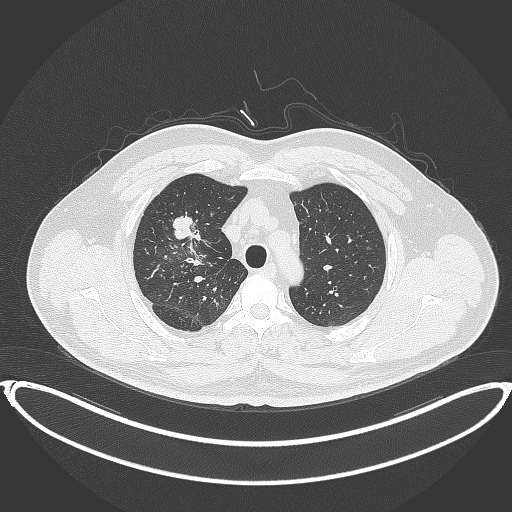
Chest CT, one axial slice; position 302 of 399 along the scan axis; 120 kVp; lung window (W 1500 / L -600 HU); 1 mm slice thickness; 512 × 512 image matrix, field of view 445 × 445 mm. Patient: male, 53 years. Case-level facts recorded for this patient, not image findings: clinical TNM (as recorded): T2a N0 M0.
Annotated regions visible in this slice (rectangle marked by the reading radiologist):
- lung tumour (recorded histology: adenocarcinoma): box from (x=168, y=213) to (x=206, y=248) px